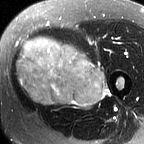
MRI of an extremity soft-tissue mass, one axial slice; slice 27 of 60 in the series (ordered by position); T2-weighted fat-saturated; MR volume resampled by the dataset authors to the PET/CT grid (not the native acquisition matrix); 144 × 144 image matrix, field of view 141 × 141 mm. Female patient. Case-level facts recorded for this patient, not image findings: histological type: pleiomorphic leiomyosarcoma; grade: intermediate; site of the primary tumour: left thigh.
Structures marked on this image (expert contour drawn on MRI and transferred to this co-registered scan by the dataset authors):
- gross tumour volume including surrounding oedema: bounding box (x1, y1, x2, y2) in pixels: (15, 38, 110, 111)
- gross tumour volume (mass): (15, 38, 105, 107)